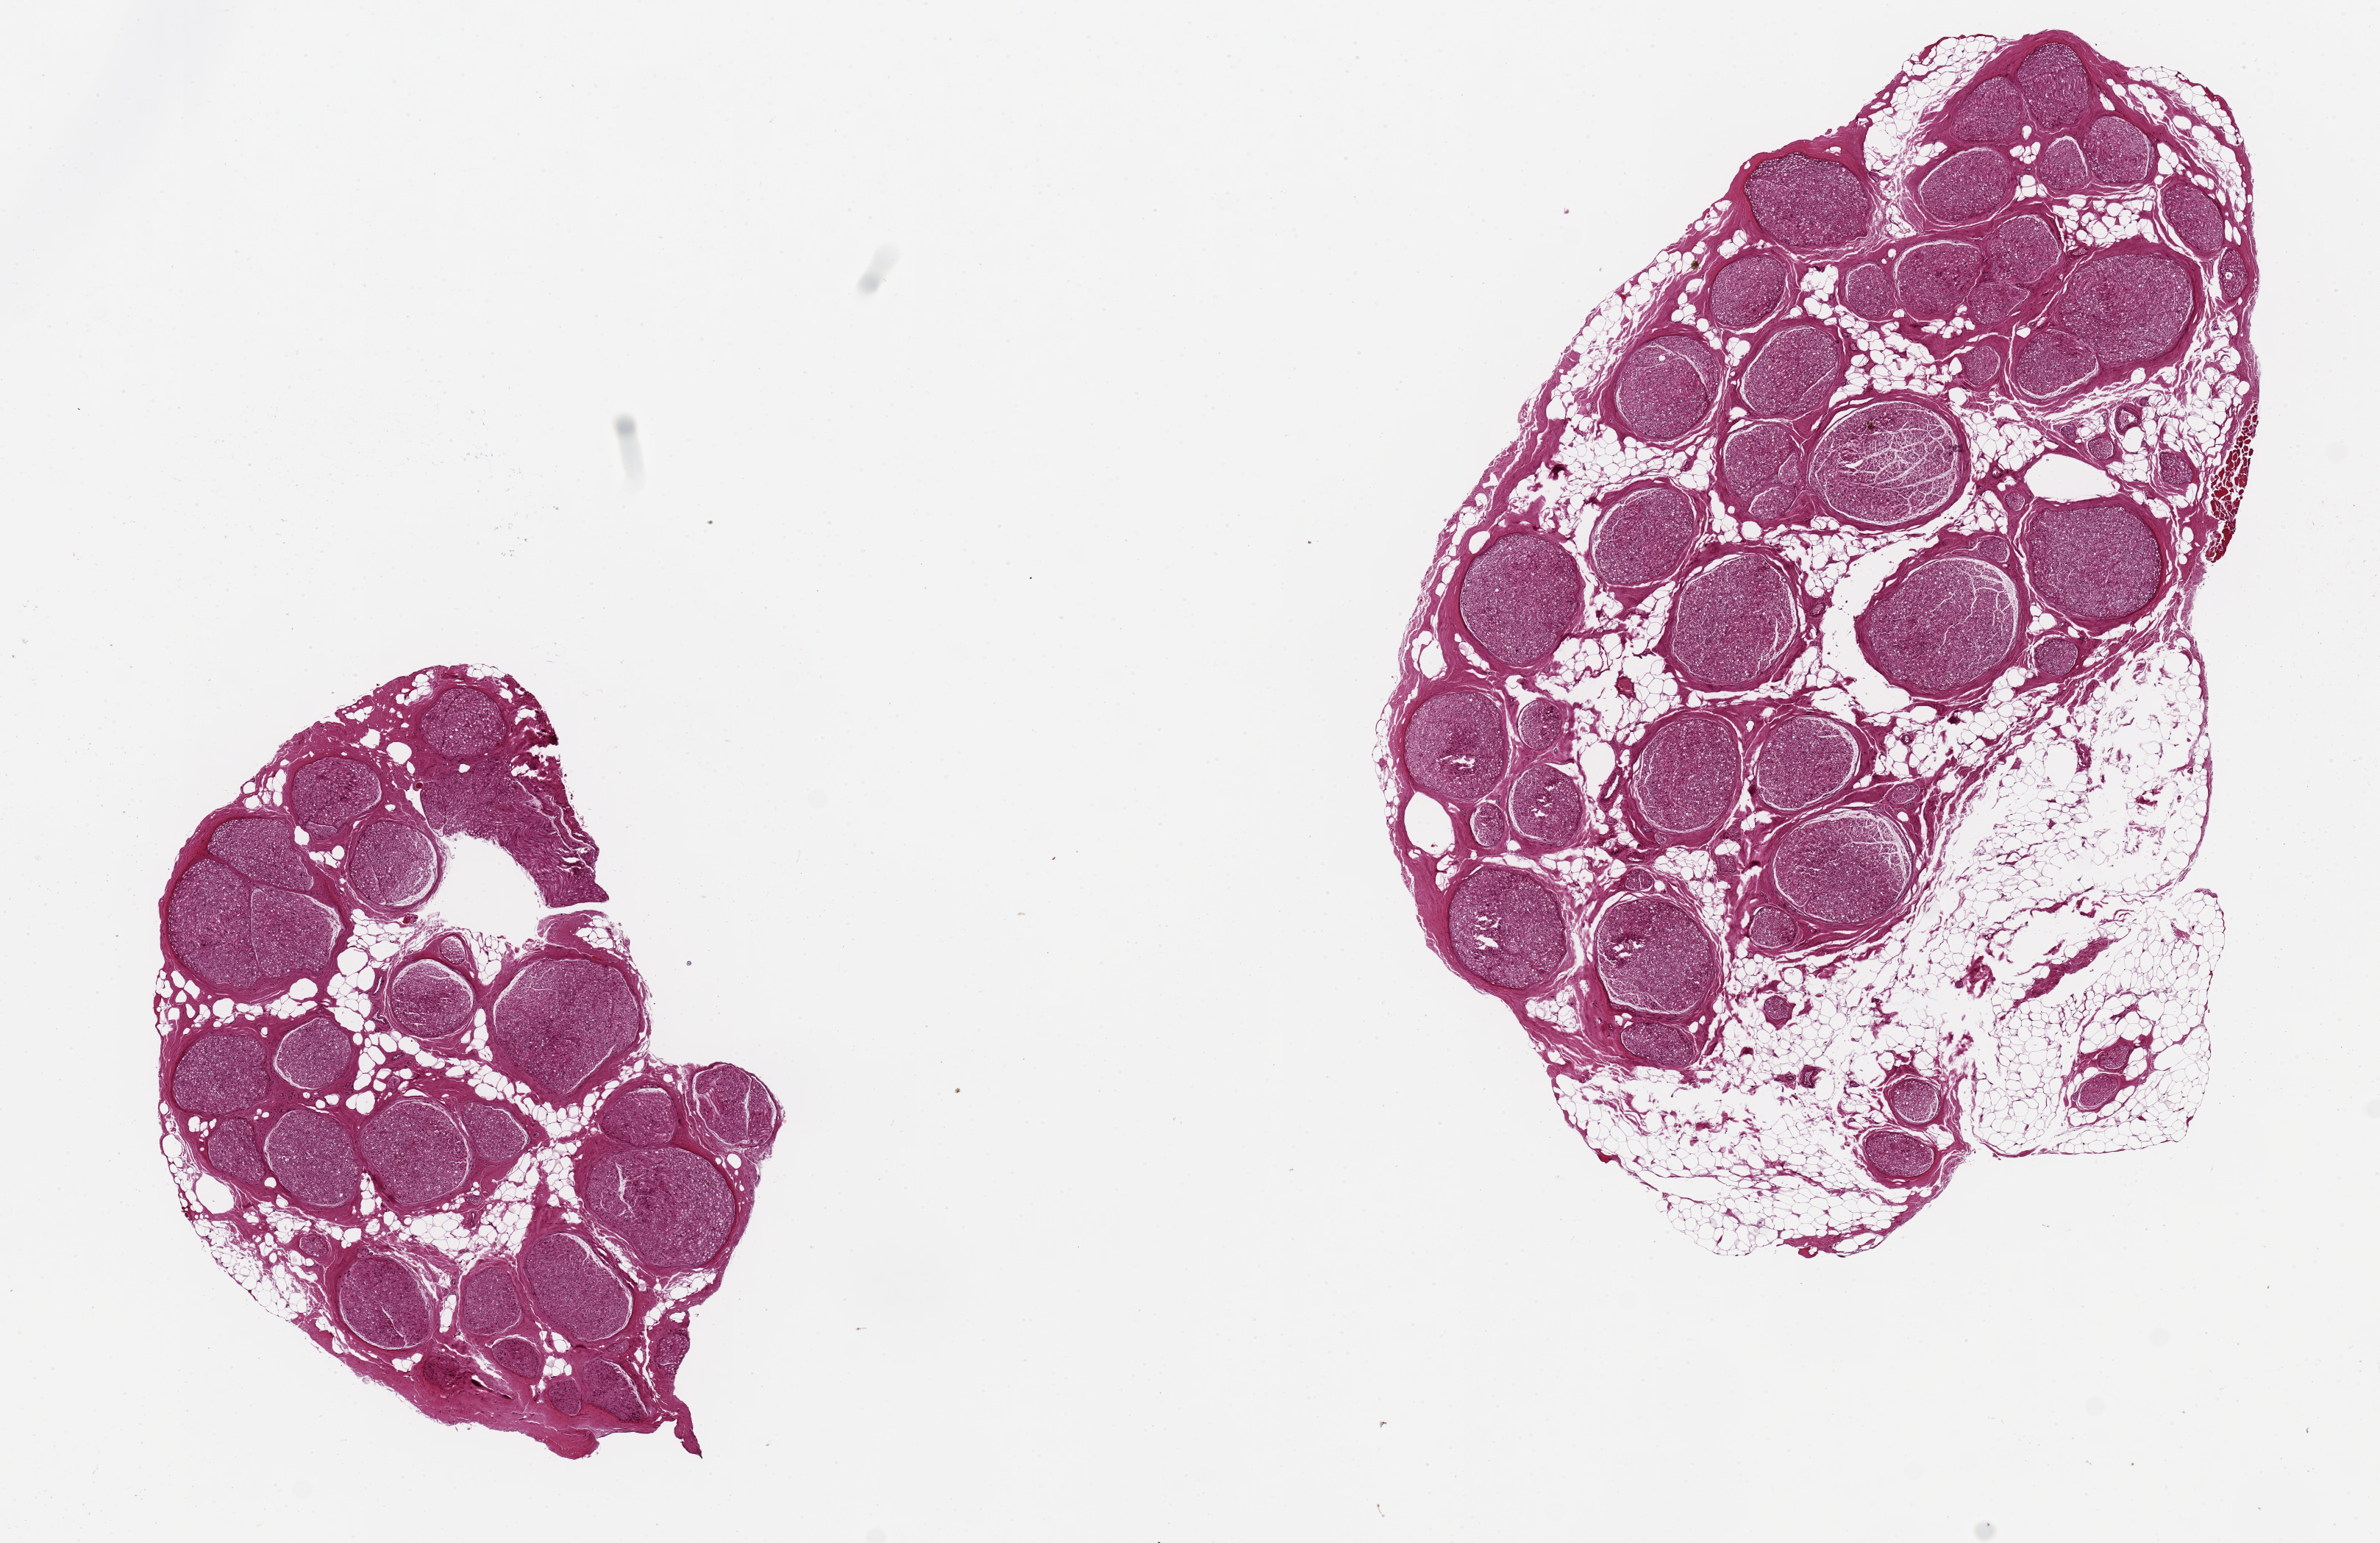
Digitized H&E-stained section, shown as a low-resolution overview of the whole scanned area (about 12.8 x 8.3 mm); PAXgene-fixed, paraffin-embedded tissue; target tissue: tibial nerve; donor tissue sample. Female donor.
- review note (as recorded): 2 aliquots, ~5x3mm, moderate interstitial fat, ~30% of specimens